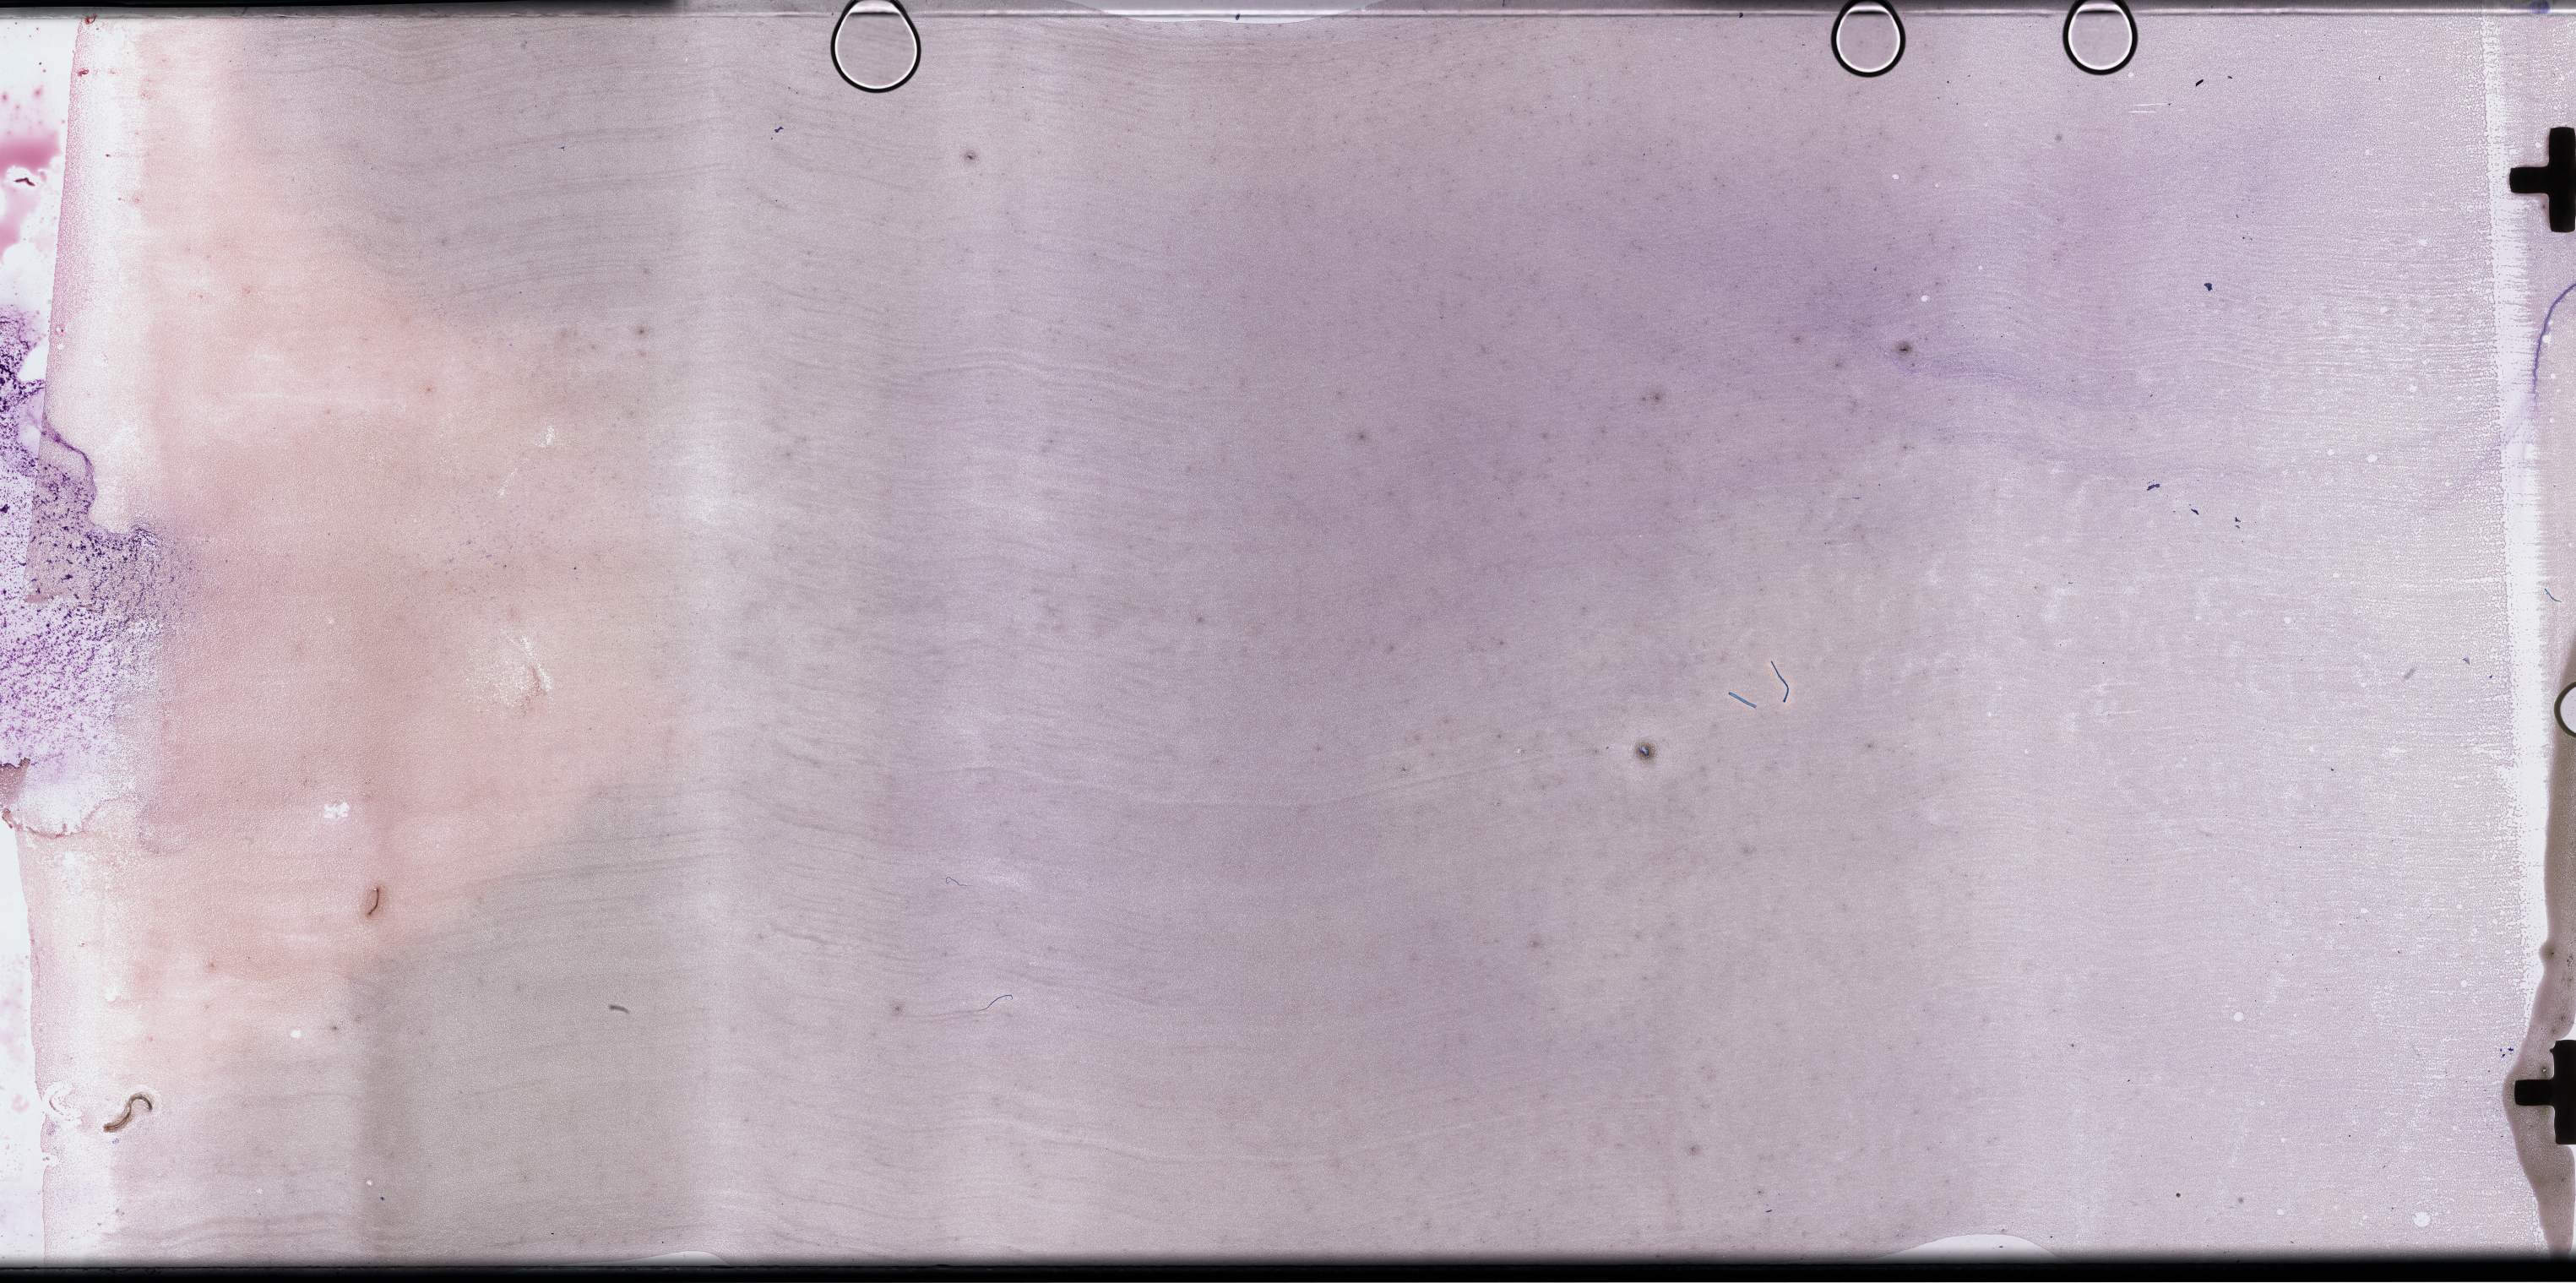
Wright–Giemsa-stained whole blood smear, whole-slide image, shown as a low-resolution overview of the whole scanned area (about 49.3 x 24.5 mm). EDTA-anticoagulated smear. Specimen time point: collected at disease progression. Male patient.
From a patient with: Plasma Cell Myeloma.